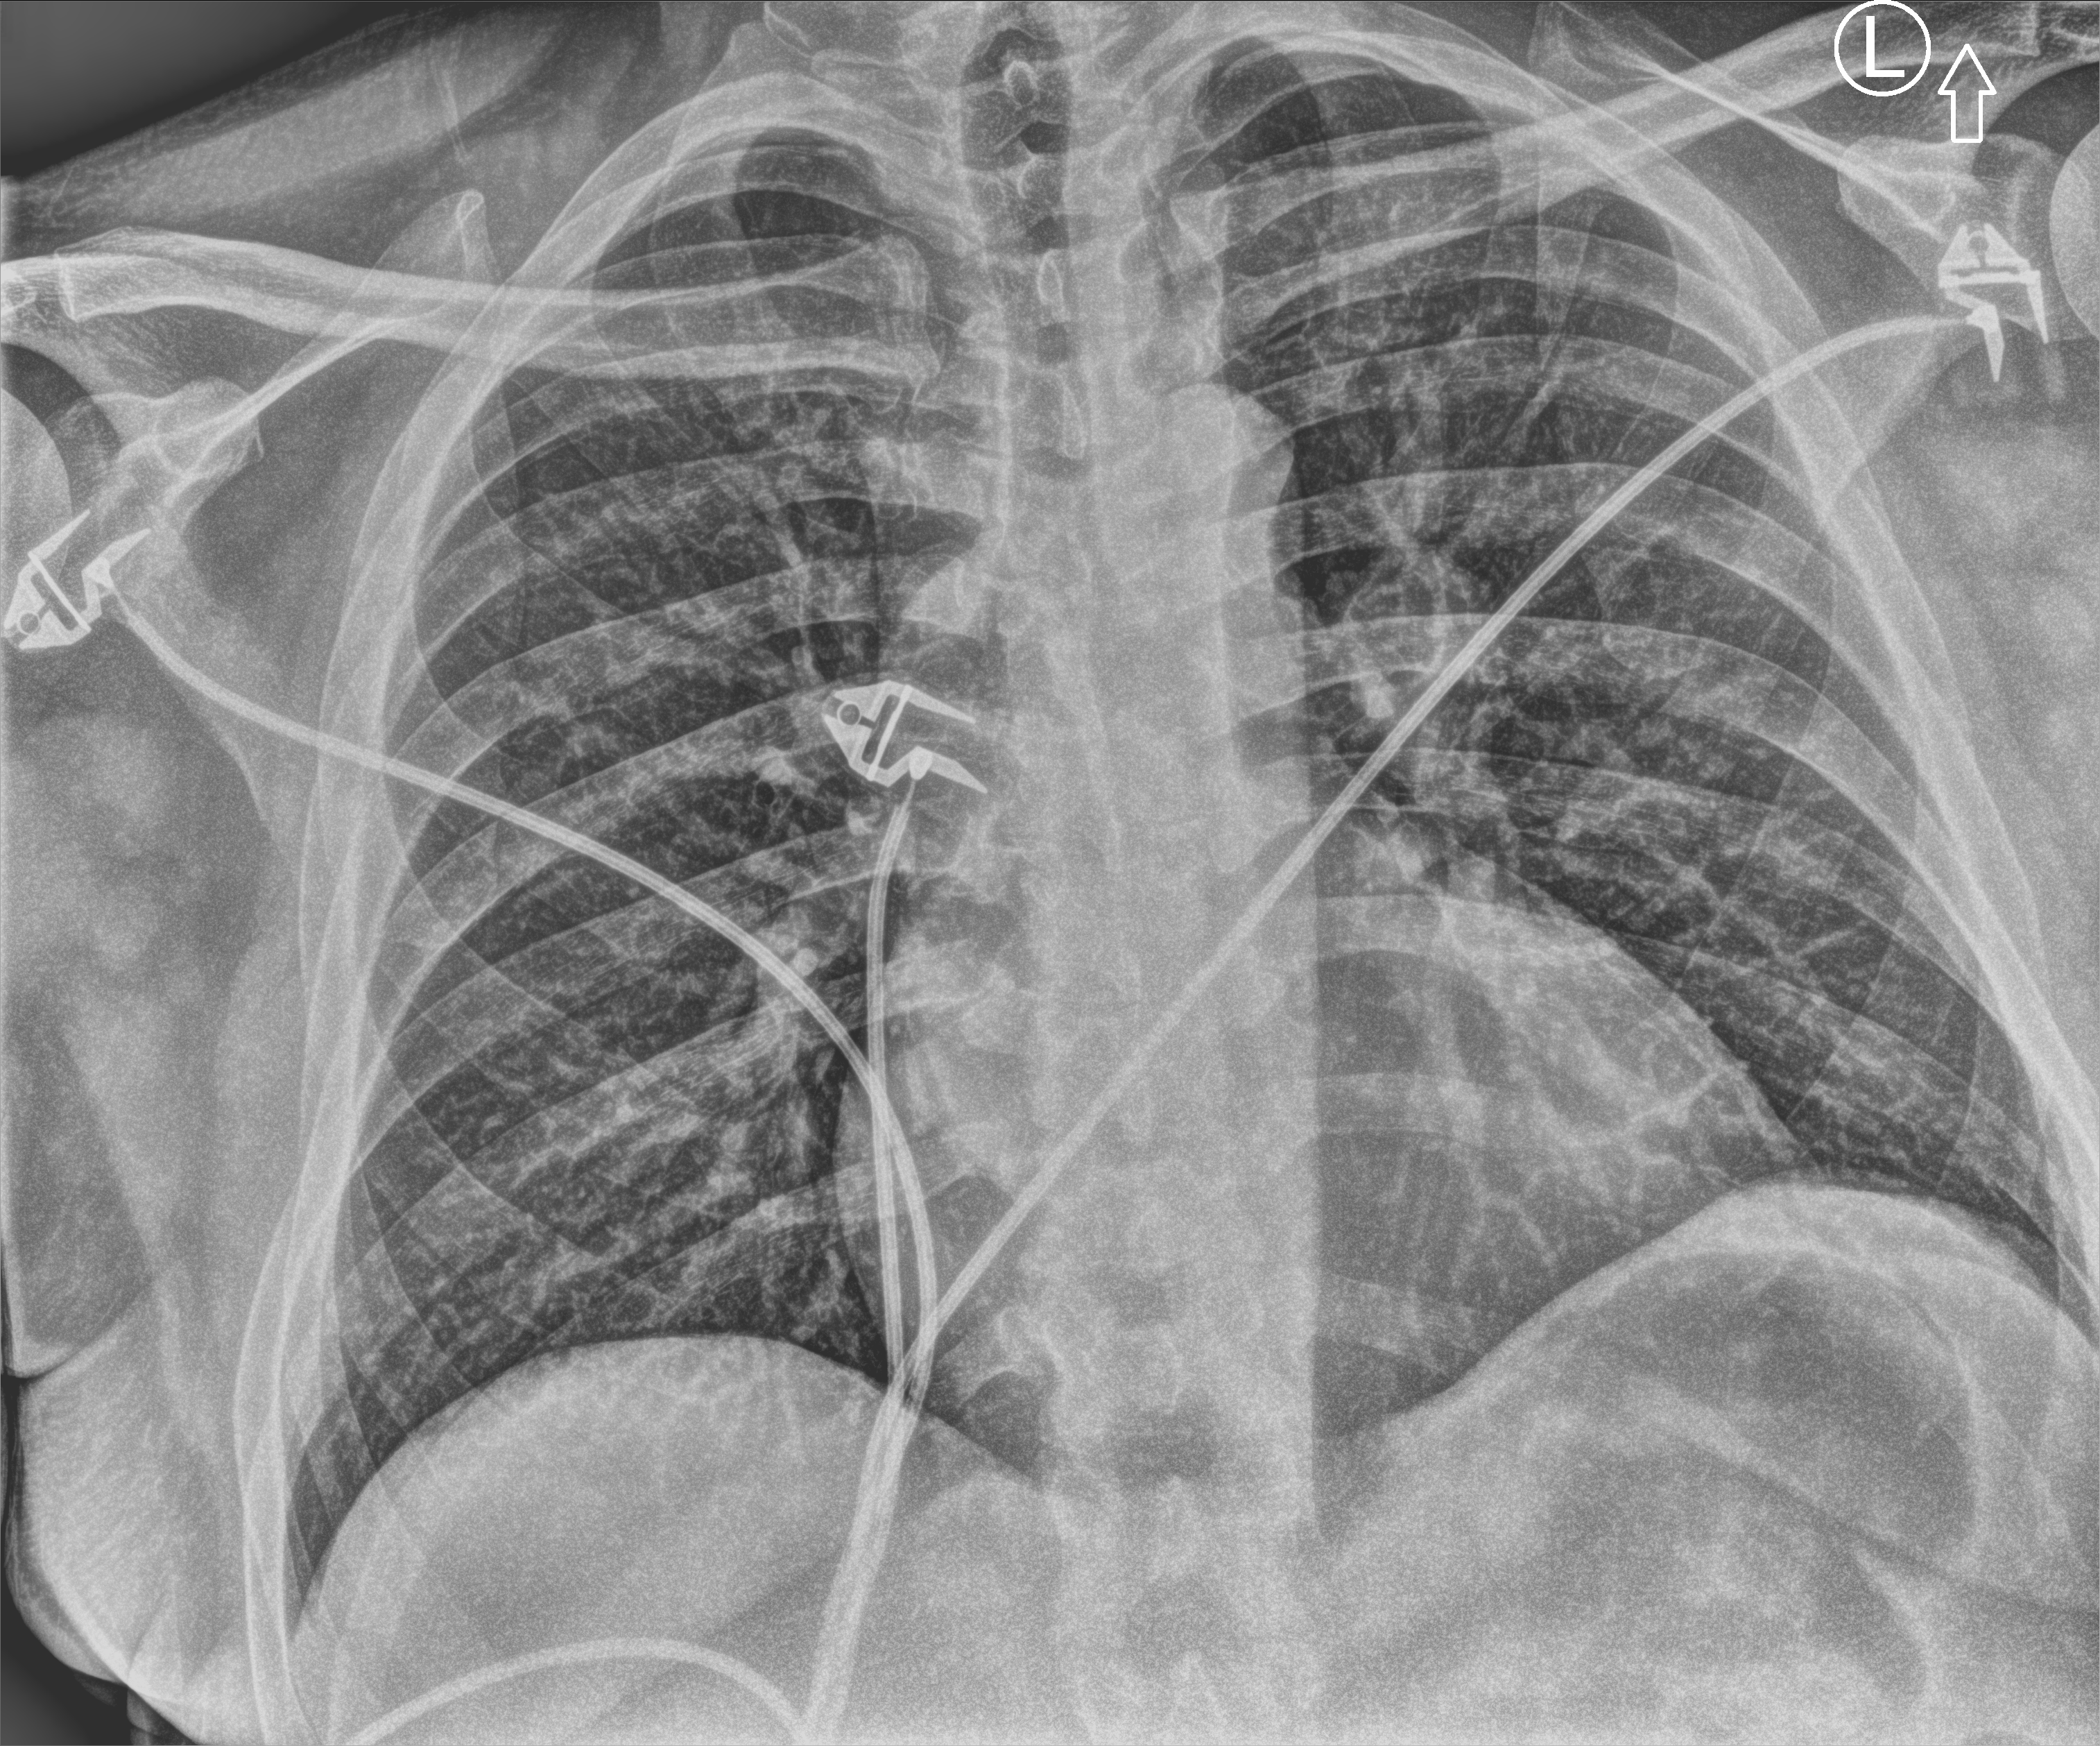
Chest X-ray (portable); anteroposterior (AP) projection. Male patient hospitalised with COVID-19, age 18–59 years.
Hospital-stay facts (about this admission, not read from this image; timing relative to this image not recorded):
- hypertension (admission record): yes
- length of hospital stay: 36 days
- admitted to intensive care during this hospital stay: no